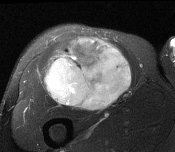
MRI of an extremity soft-tissue mass, one axial slice; T2-weighted fat-saturated; MR volume resampled by the dataset authors to the PET/CT grid (not the native acquisition matrix); 3.27 mm slice thickness; 175 × 152 image matrix. Male patient. Case-level facts recorded for this patient, not image findings: histological type: pleiomorphic leiomyosarcoma; grade: intermediate; site of the primary tumour: right thigh.
Outlined on this slice (expert contour drawn on MRI and transferred to this co-registered scan by the dataset authors):
- gross tumour volume including surrounding oedema: box from (x=44, y=38) to (x=132, y=110) px
- gross tumour volume (mass): (x=45, y=38)–(x=132, y=110)